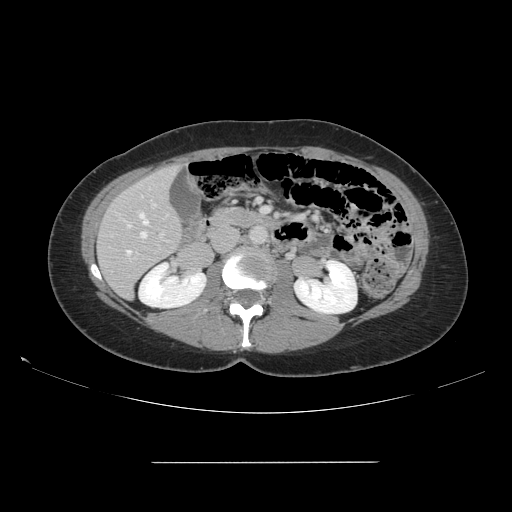
Contrast-enhanced abdominal CT, one axial slice; slice 62 of 151 in the series (ordered by position); 120 kVp; intravenous contrast given; soft-tissue window (W 400 / L 40 HU); 2.5 mm slice thickness; 512 × 512 image matrix, field of view 421 × 421 mm. Female patient, age 46 years. From the clinical record (not read from this slice): diagnosis: colorectal cancer liver metastases, imaged before liver resection; multiple liver metastases: yes; largest metastasis: 3 cm; disease in both lobes: yes.
Annotated regions visible in this slice (outlined manually by an expert reader):
- hepatic veins: box from (x=127, y=212) to (x=149, y=256) px
- liver: (x=99, y=167)–(x=182, y=297)
- planned liver remnant (the part of the liver to remain after resection): (x=99, y=166)–(x=182, y=298)
- portal vein (with intrahepatic branches): (x=129, y=200)–(x=164, y=261)